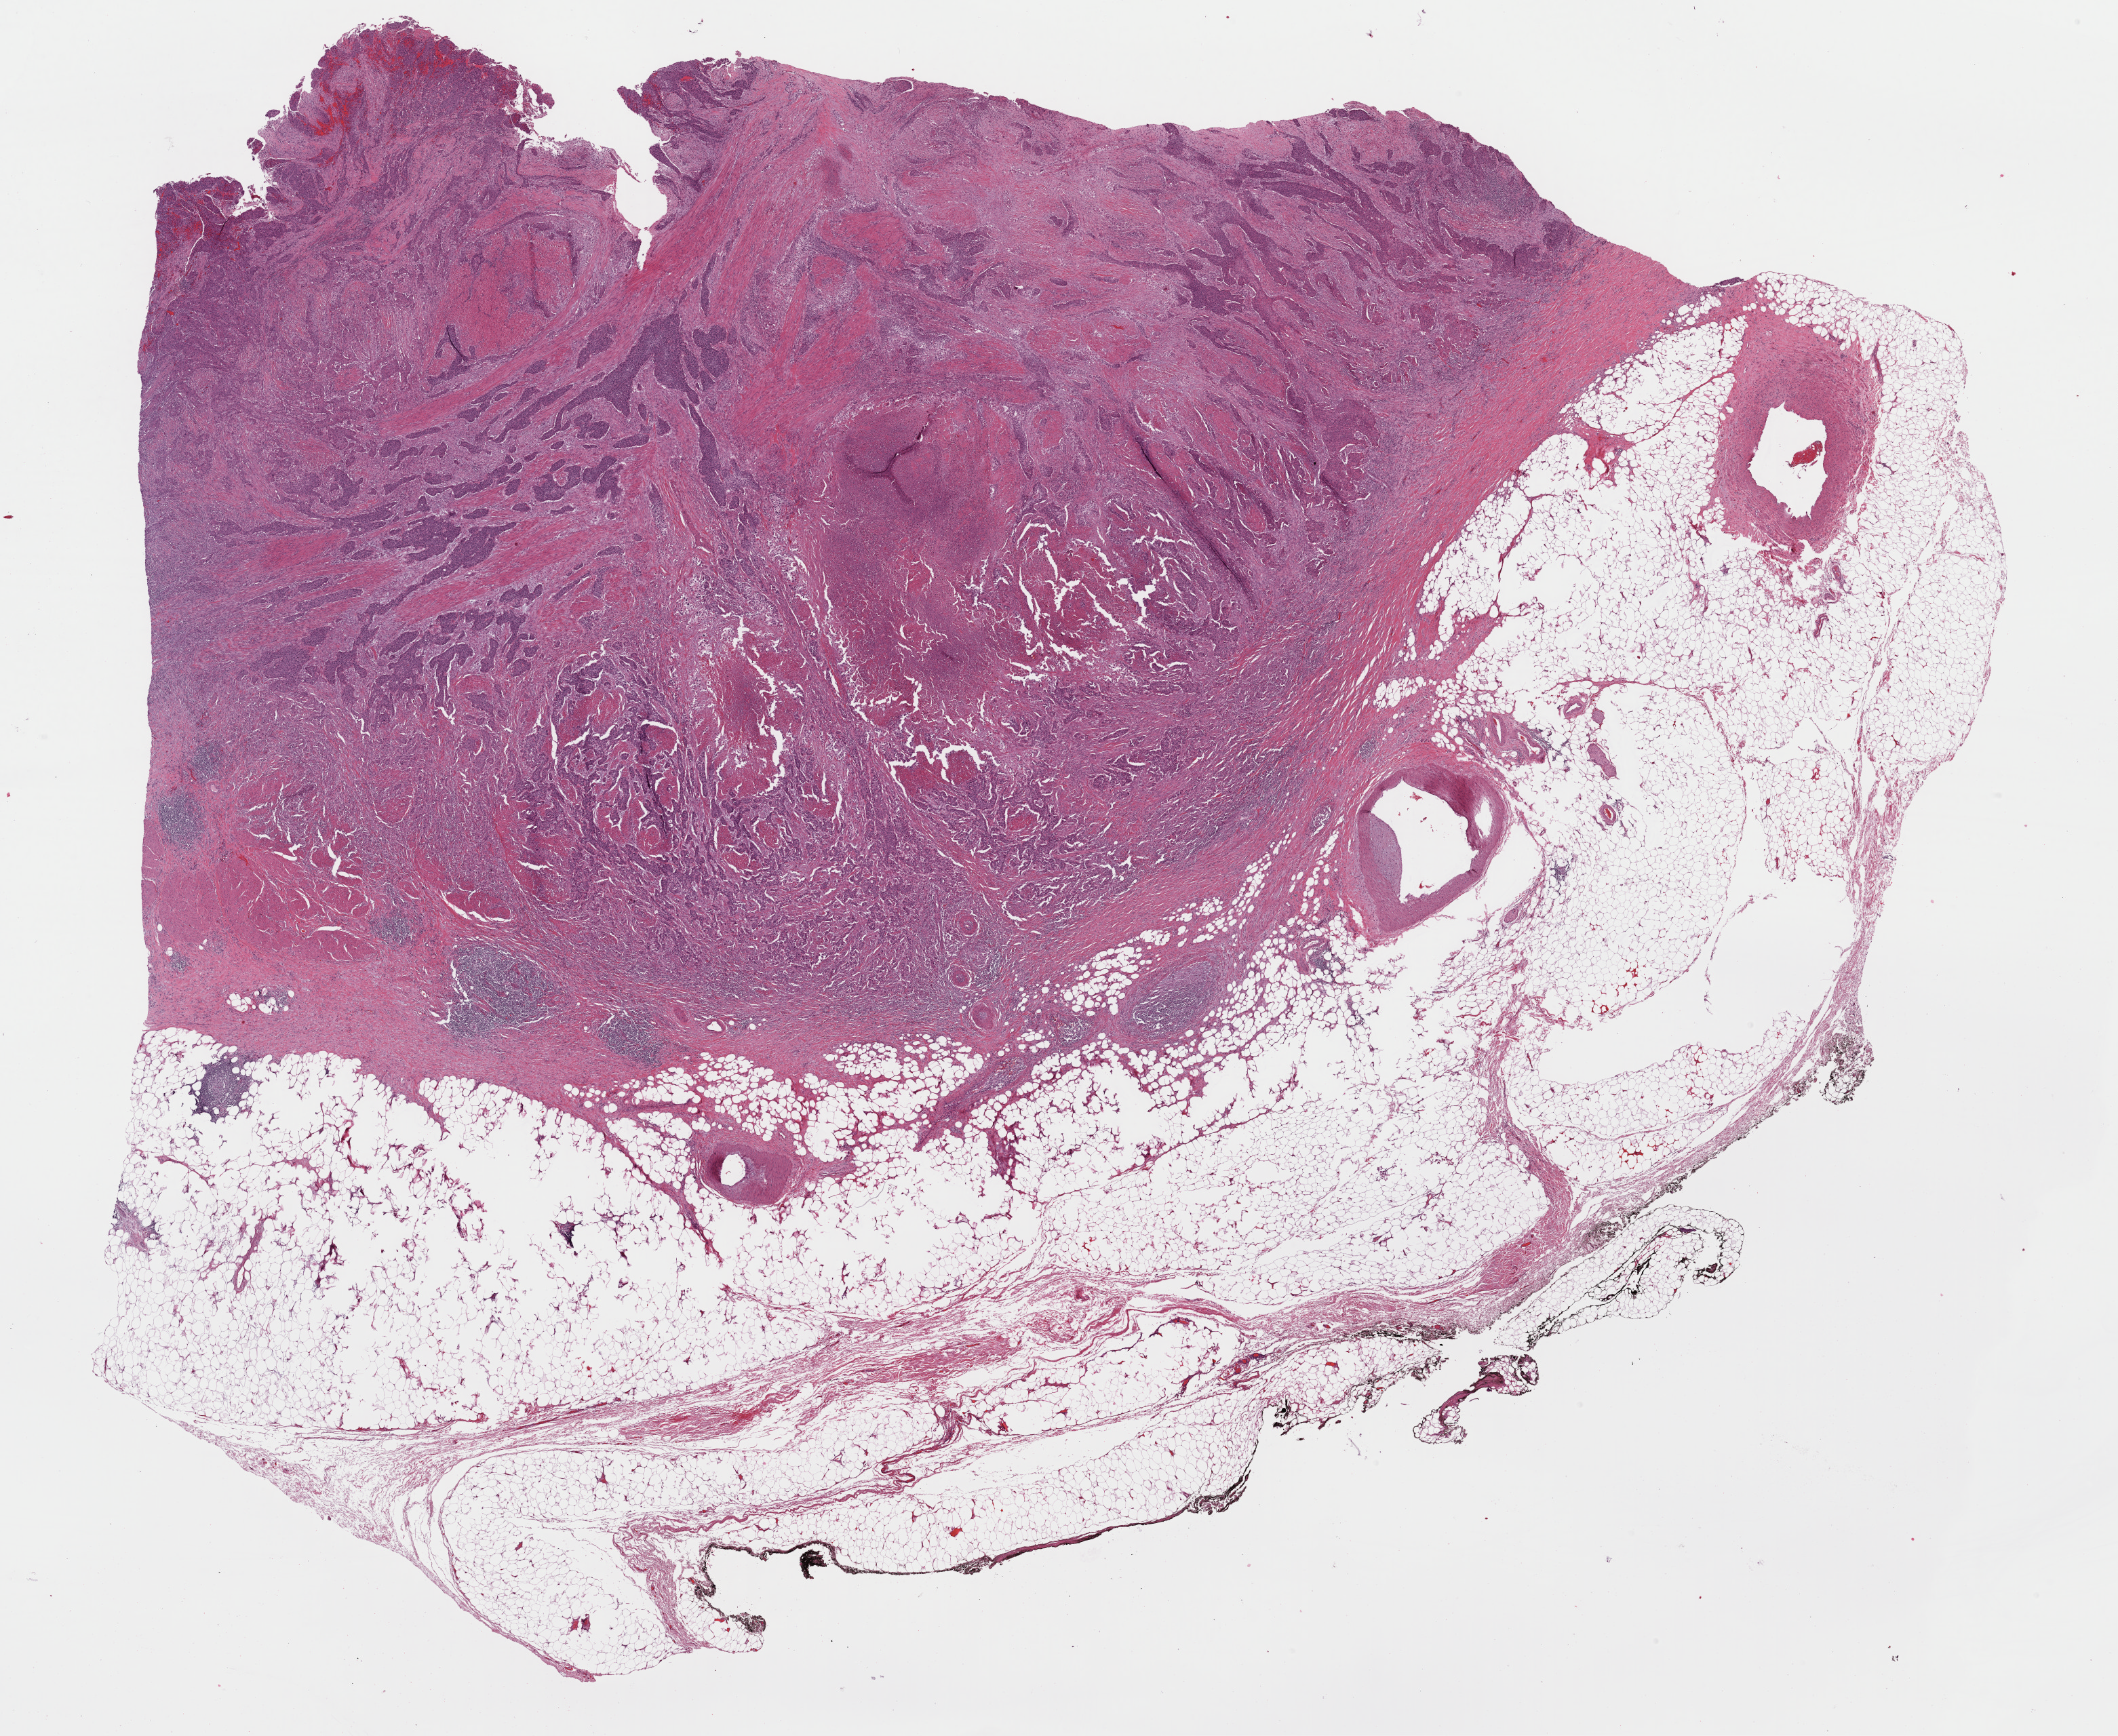
Whole-slide histology image, H&E, a low-resolution overview of the entire scanned area, about 24.7 x 20.2 mm (slide scanned at 40x); FFPE section; sample: primary tumour, bladder. Male patient; age at initial diagnosis 56 years.
Pathologic diagnosis: Transitional cell carcinoma (lateral wall of bladder).